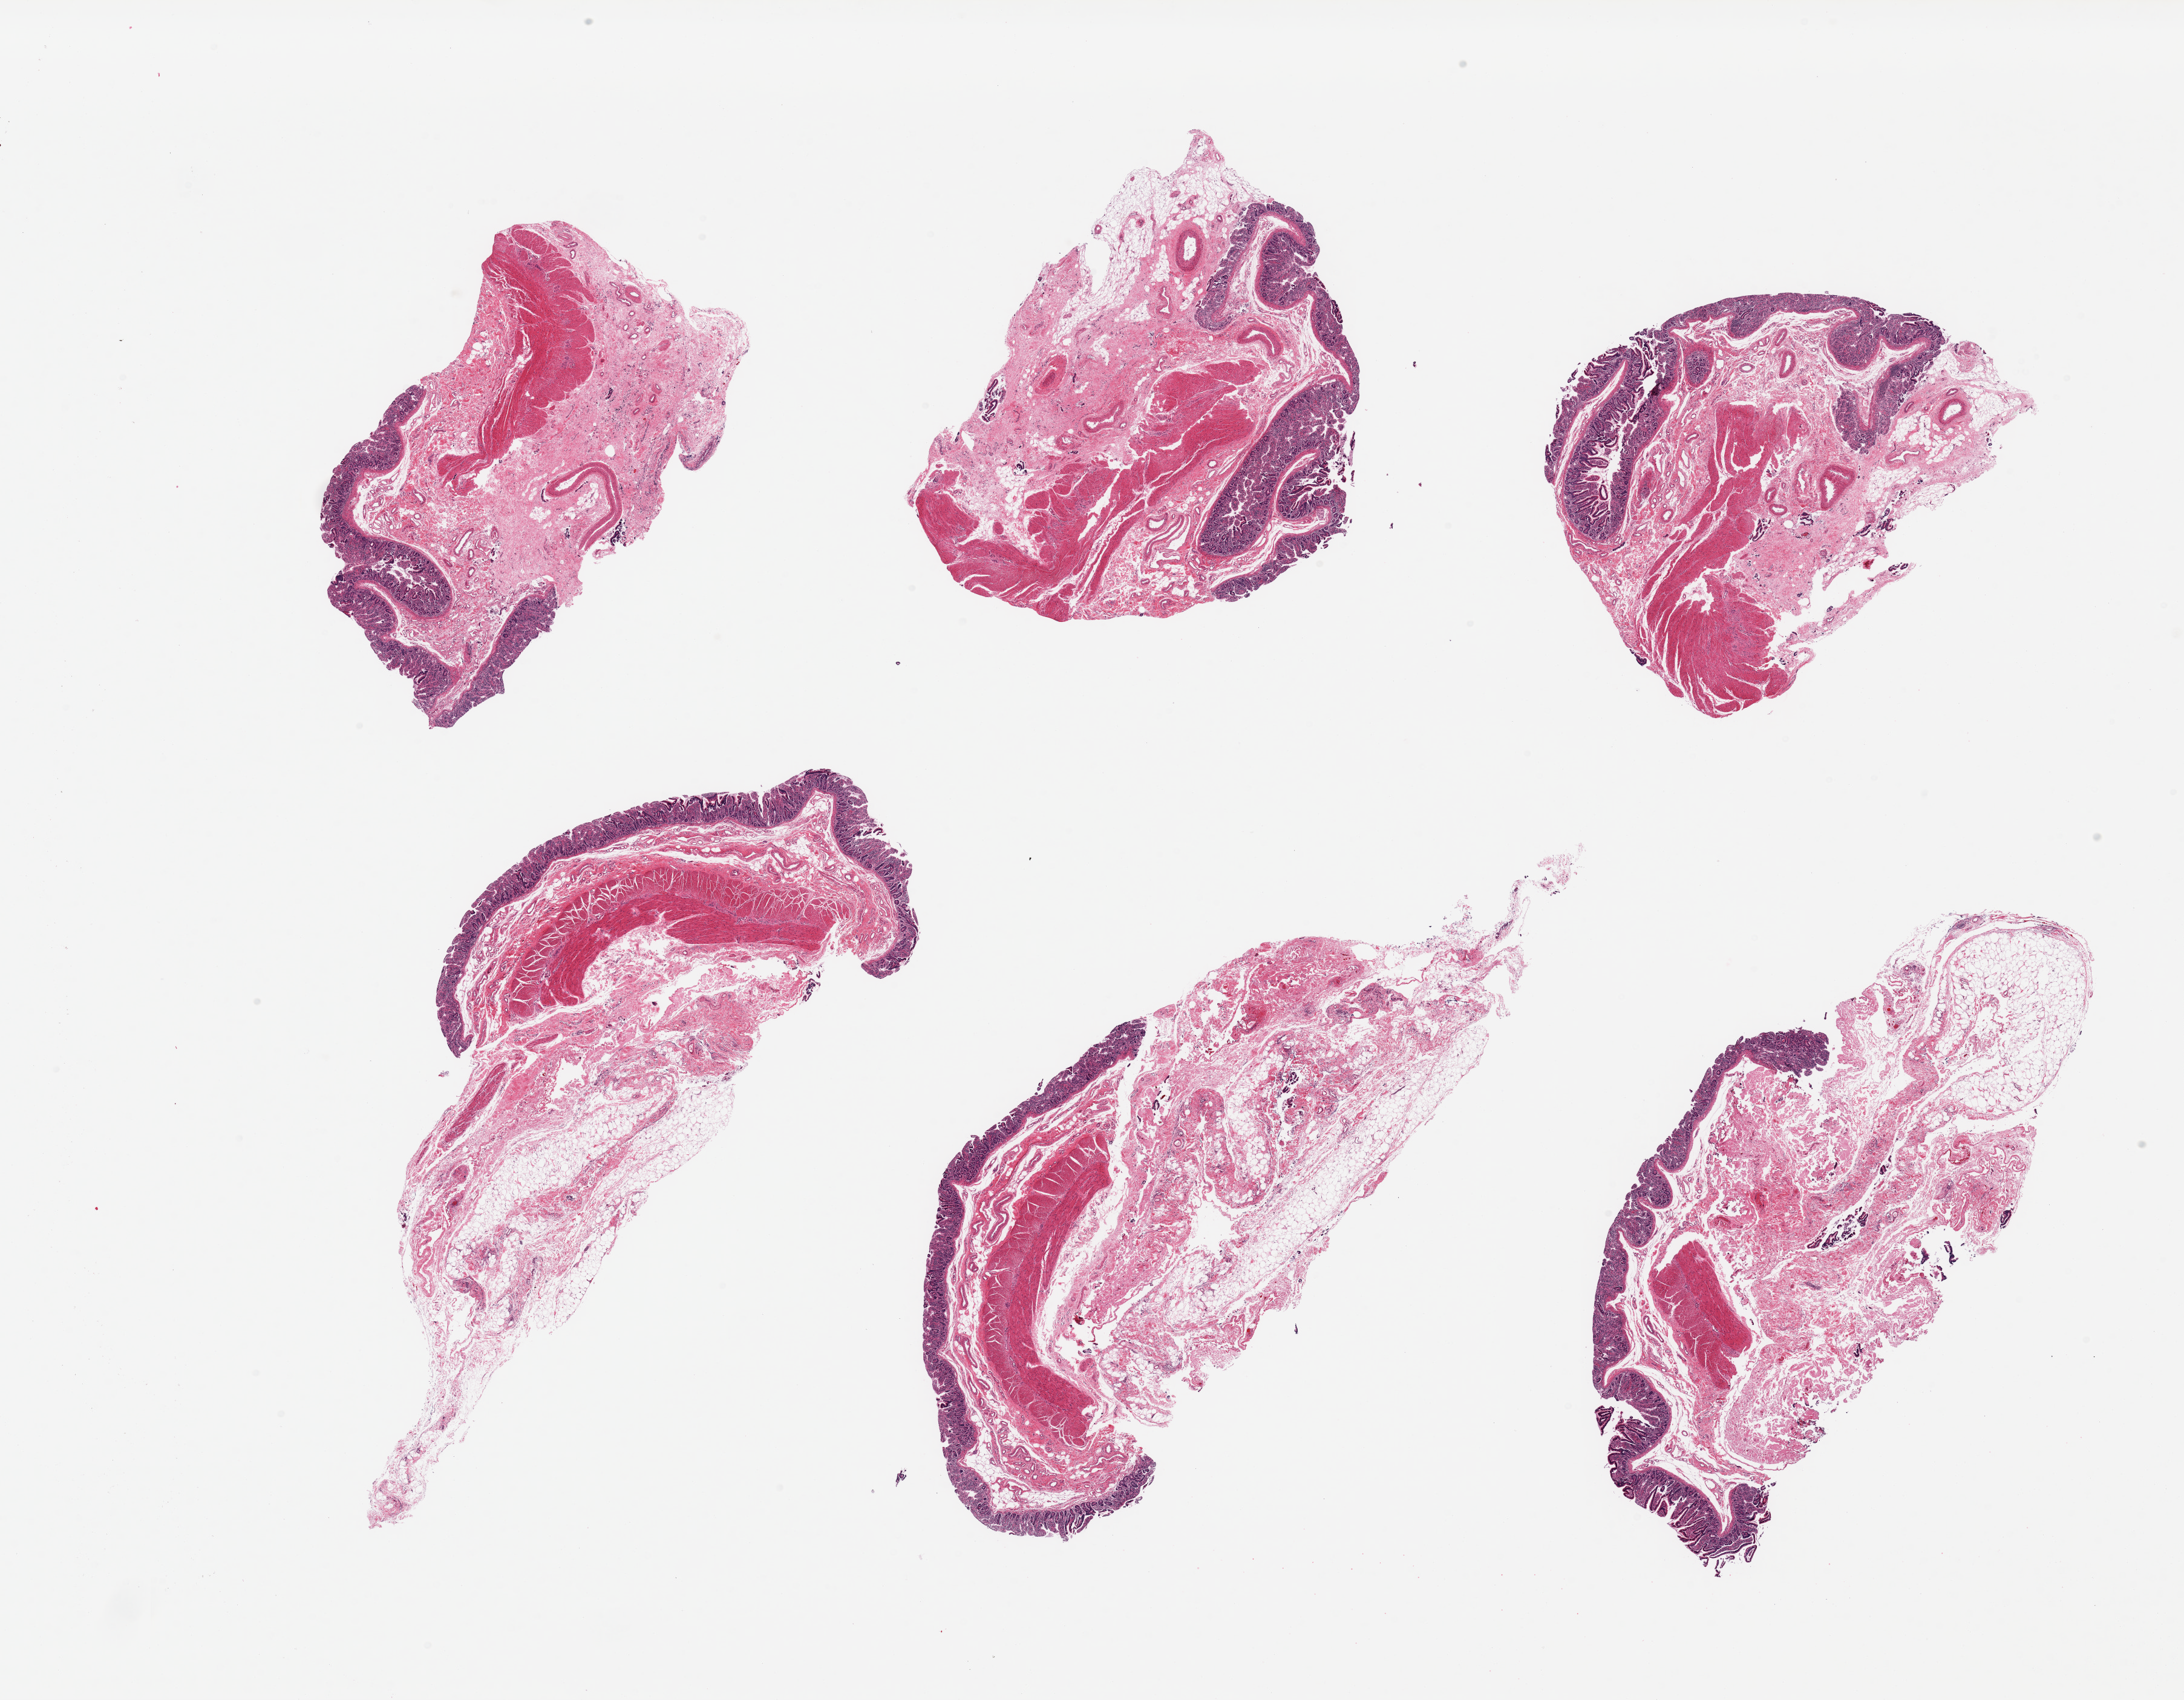
Whole-slide image, haematoxylin and eosin stain, brightfield, whole scanned area (about 28.5 x 22.2 mm) shown as a low-resolution overview; PAXgene-fixed, paraffin-embedded tissue; section of transverse colon (target tissue); donor tissue sample. Female donor.
- review note (as recorded): 6 pieces; mild to moderate autolysis of mucosa; attached serosa and fat